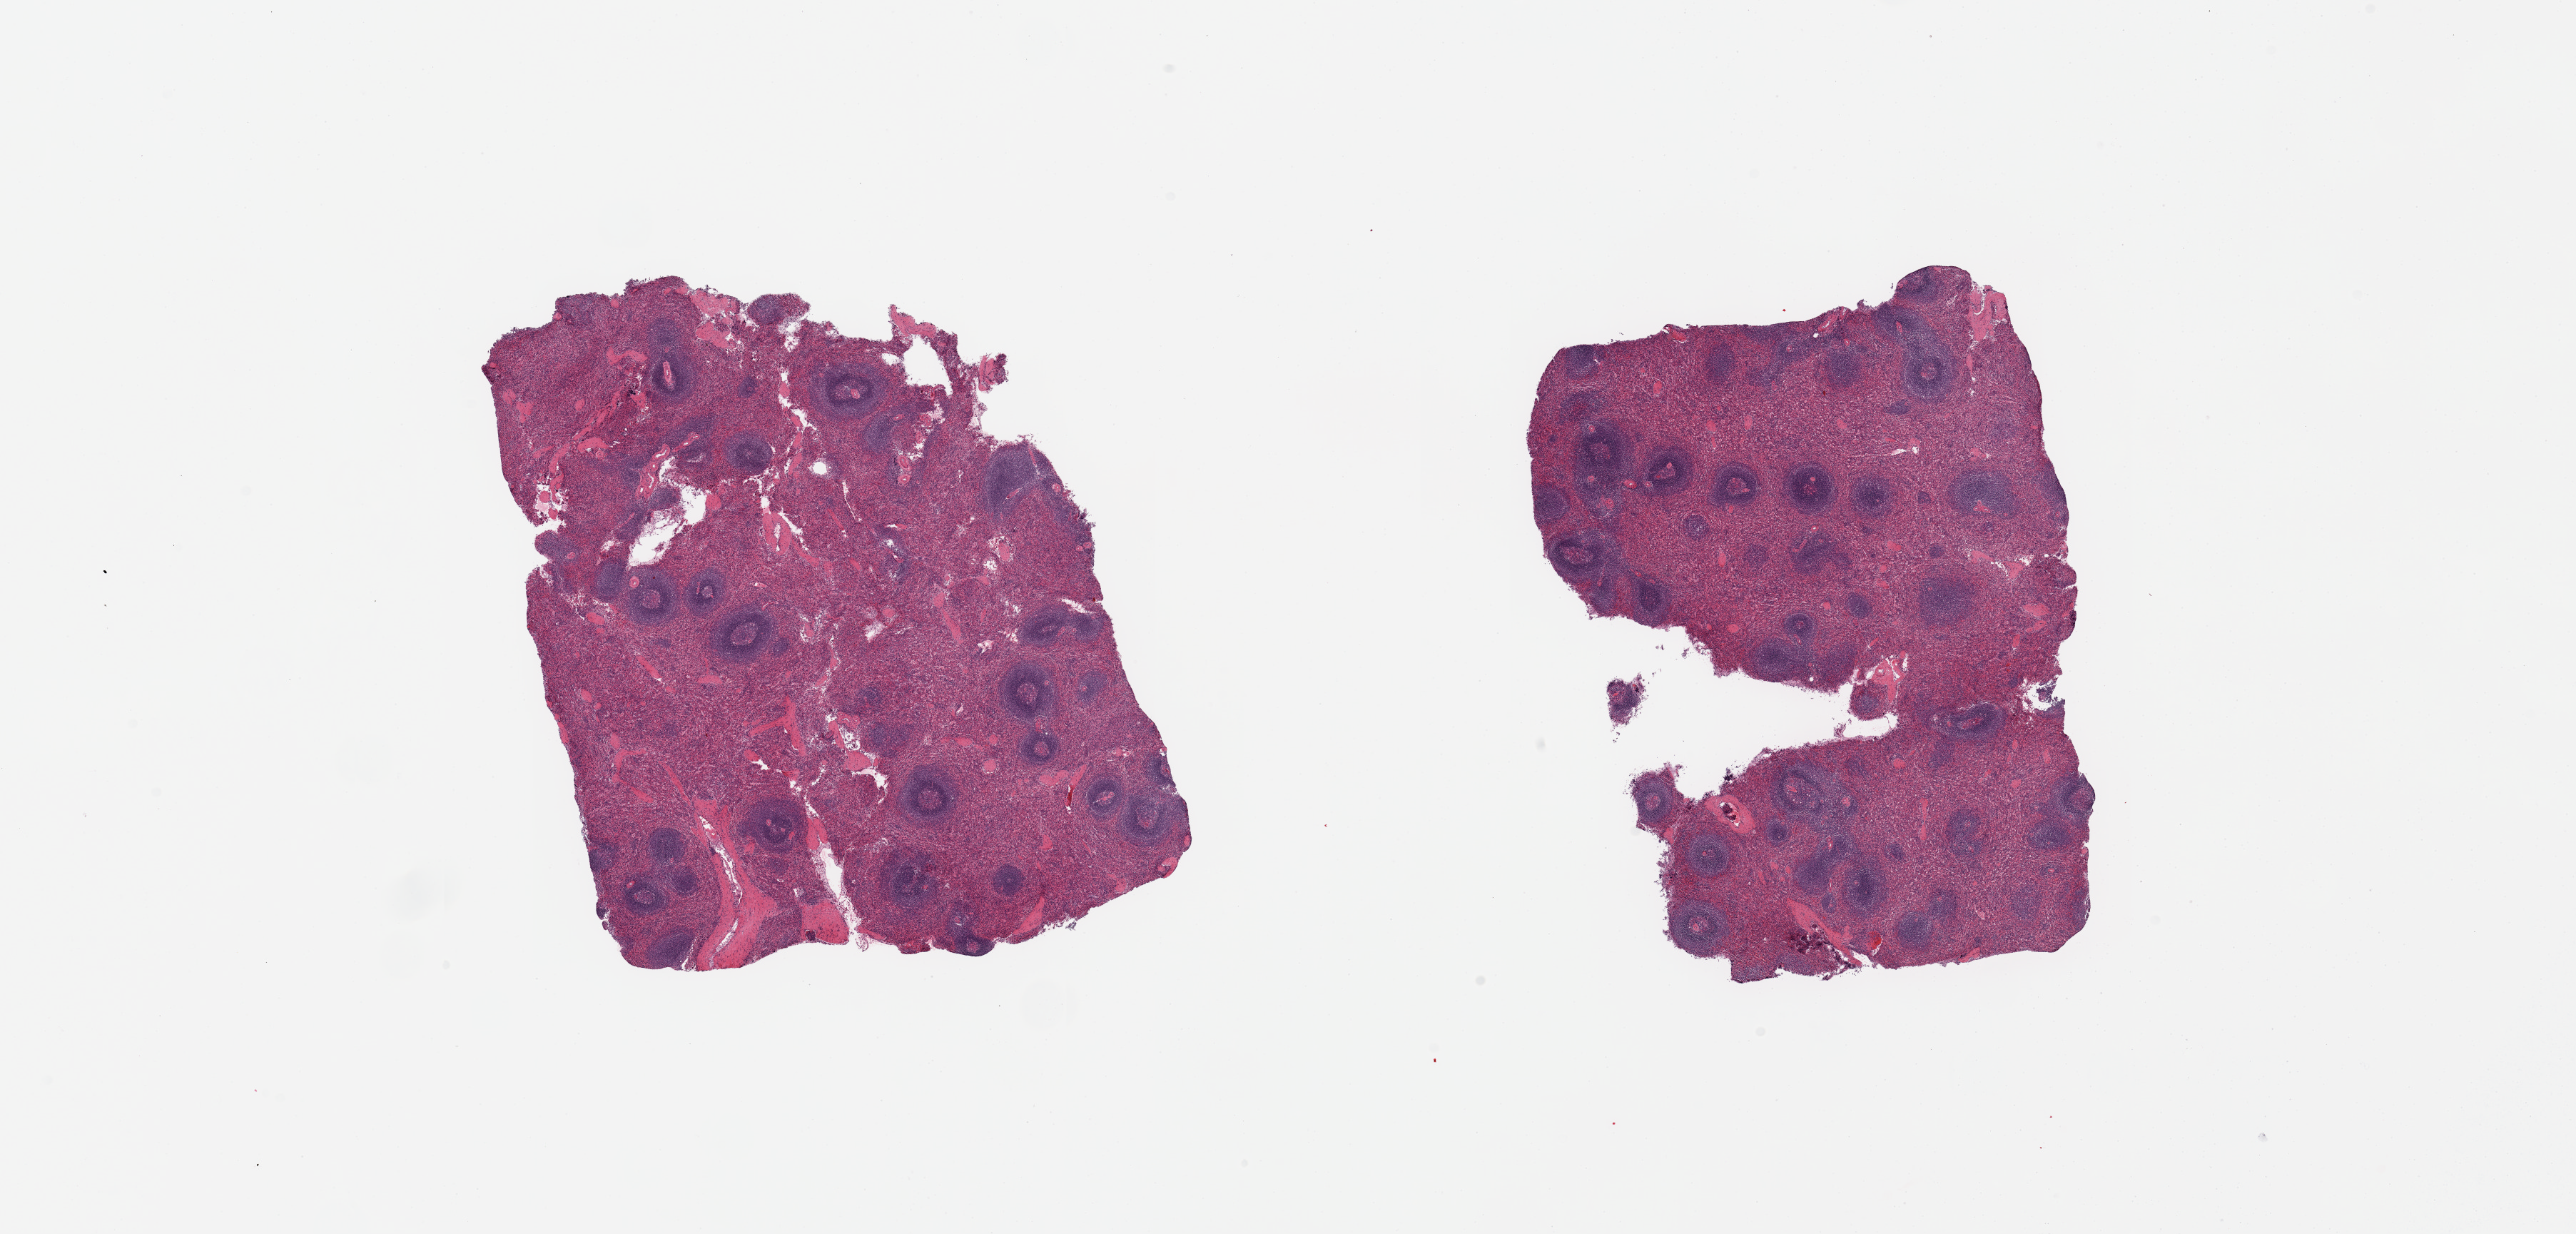
Hematoxylin and eosin (H&E) whole-slide image, shown as a low-resolution overview of the whole scanned area (about 28.5 x 13.7 mm, from a 20x scan). PAXgene-fixed paraffin-embedded (PFPE) section. Target tissue: spleen. Donor tissue sample.
• review note (as recorded): 2 pieces